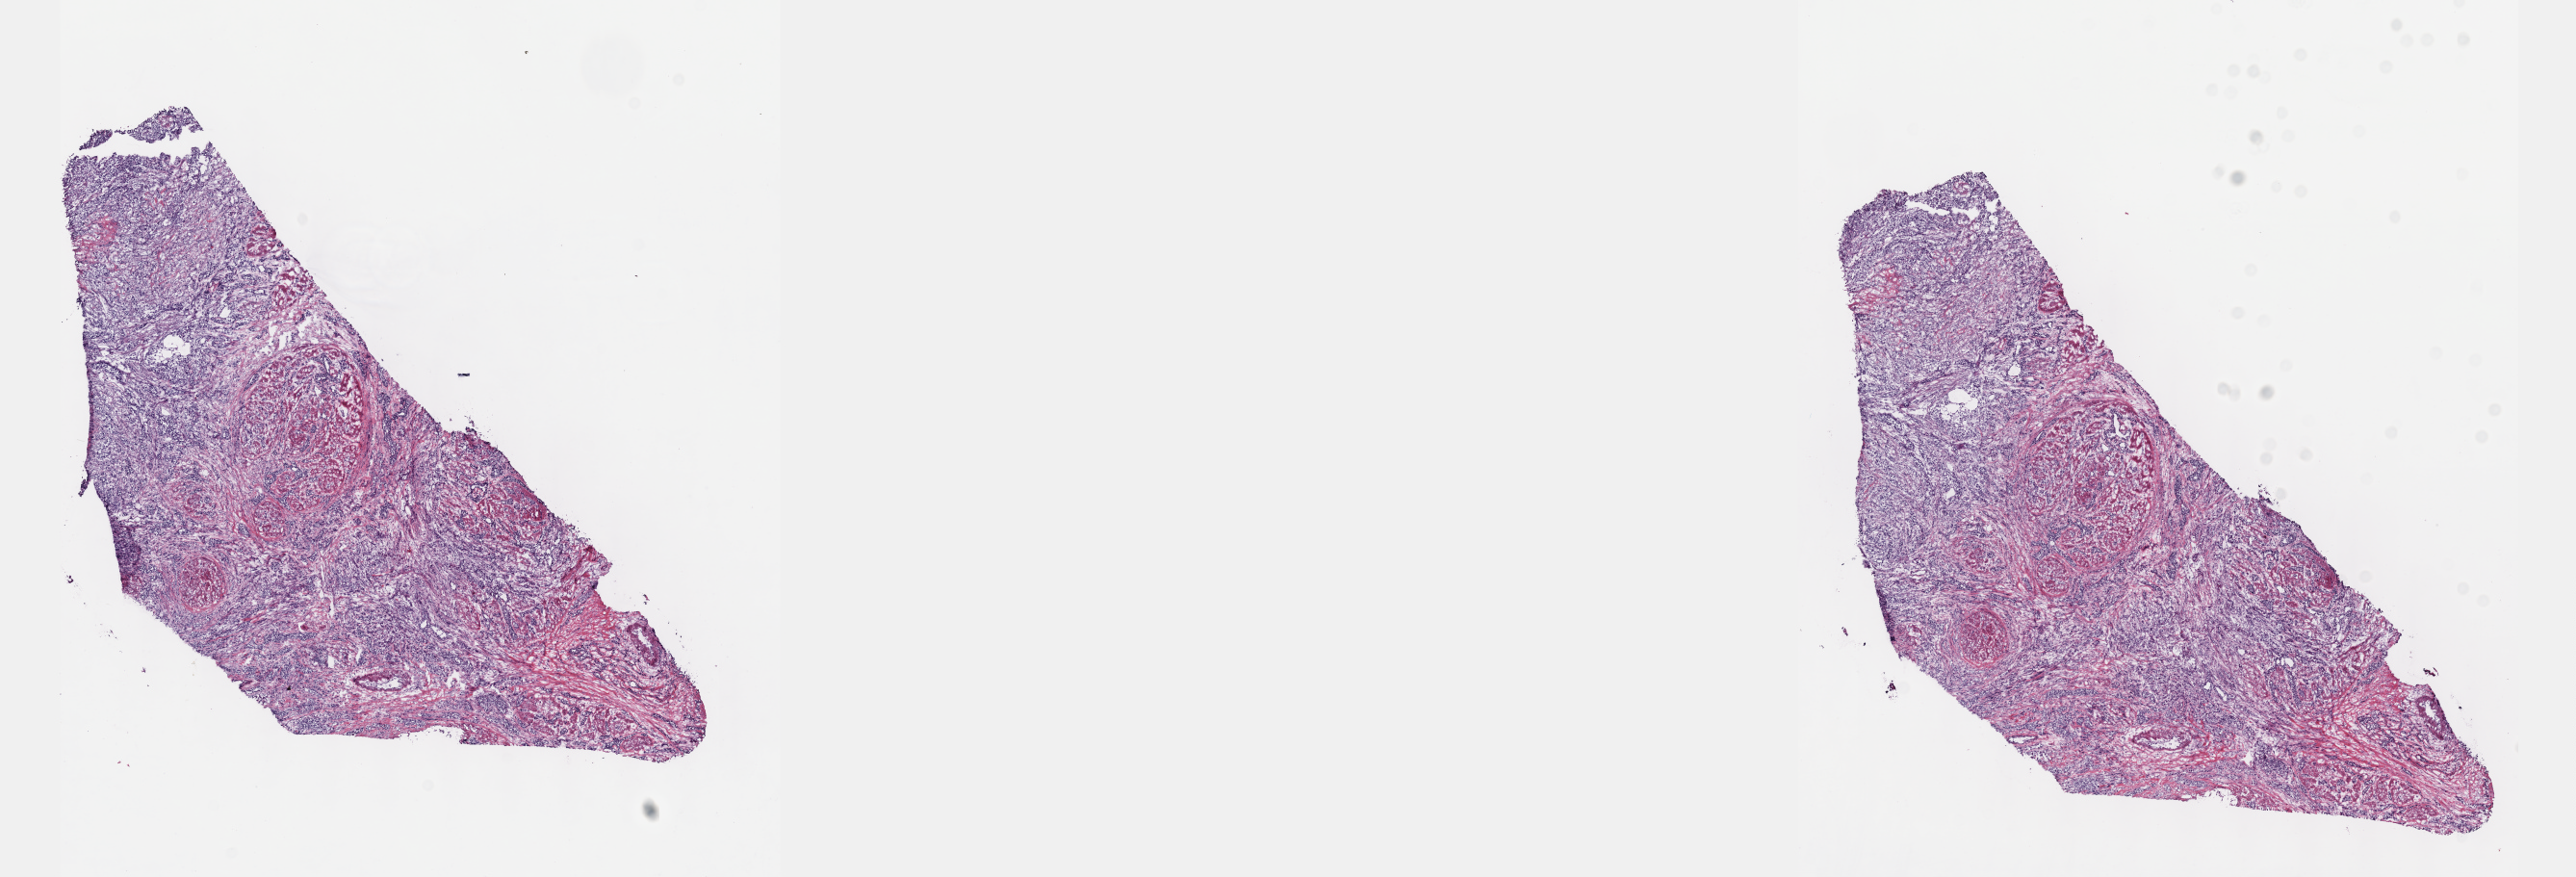
Digitized H&E tissue section (whole slide) — a low-resolution overview of the entire scanned area, about 21.6 x 7.4 mm (from a 40x scan). Frozen section from the top of the tissue portion. Bladder, primary tumour sample. Patient: female, age at initial diagnosis 75 years. Histologic grade: high grade. Pathologist review of this section (percent, as recorded): tumour cells 100%, tumour nuclei 65%, normal cells 0%, stromal cells 0%, necrosis 0%. Infiltration values recorded for this section: lymphocyte infiltration 3%, monocyte infiltration 0%, neutrophil infiltration 0%.
Pathologic diagnosis: Transitional cell carcinoma. Lymph nodes positive (case pathology): 5 of 74 examined. AJCC pathologic stage: IV (5th edition).